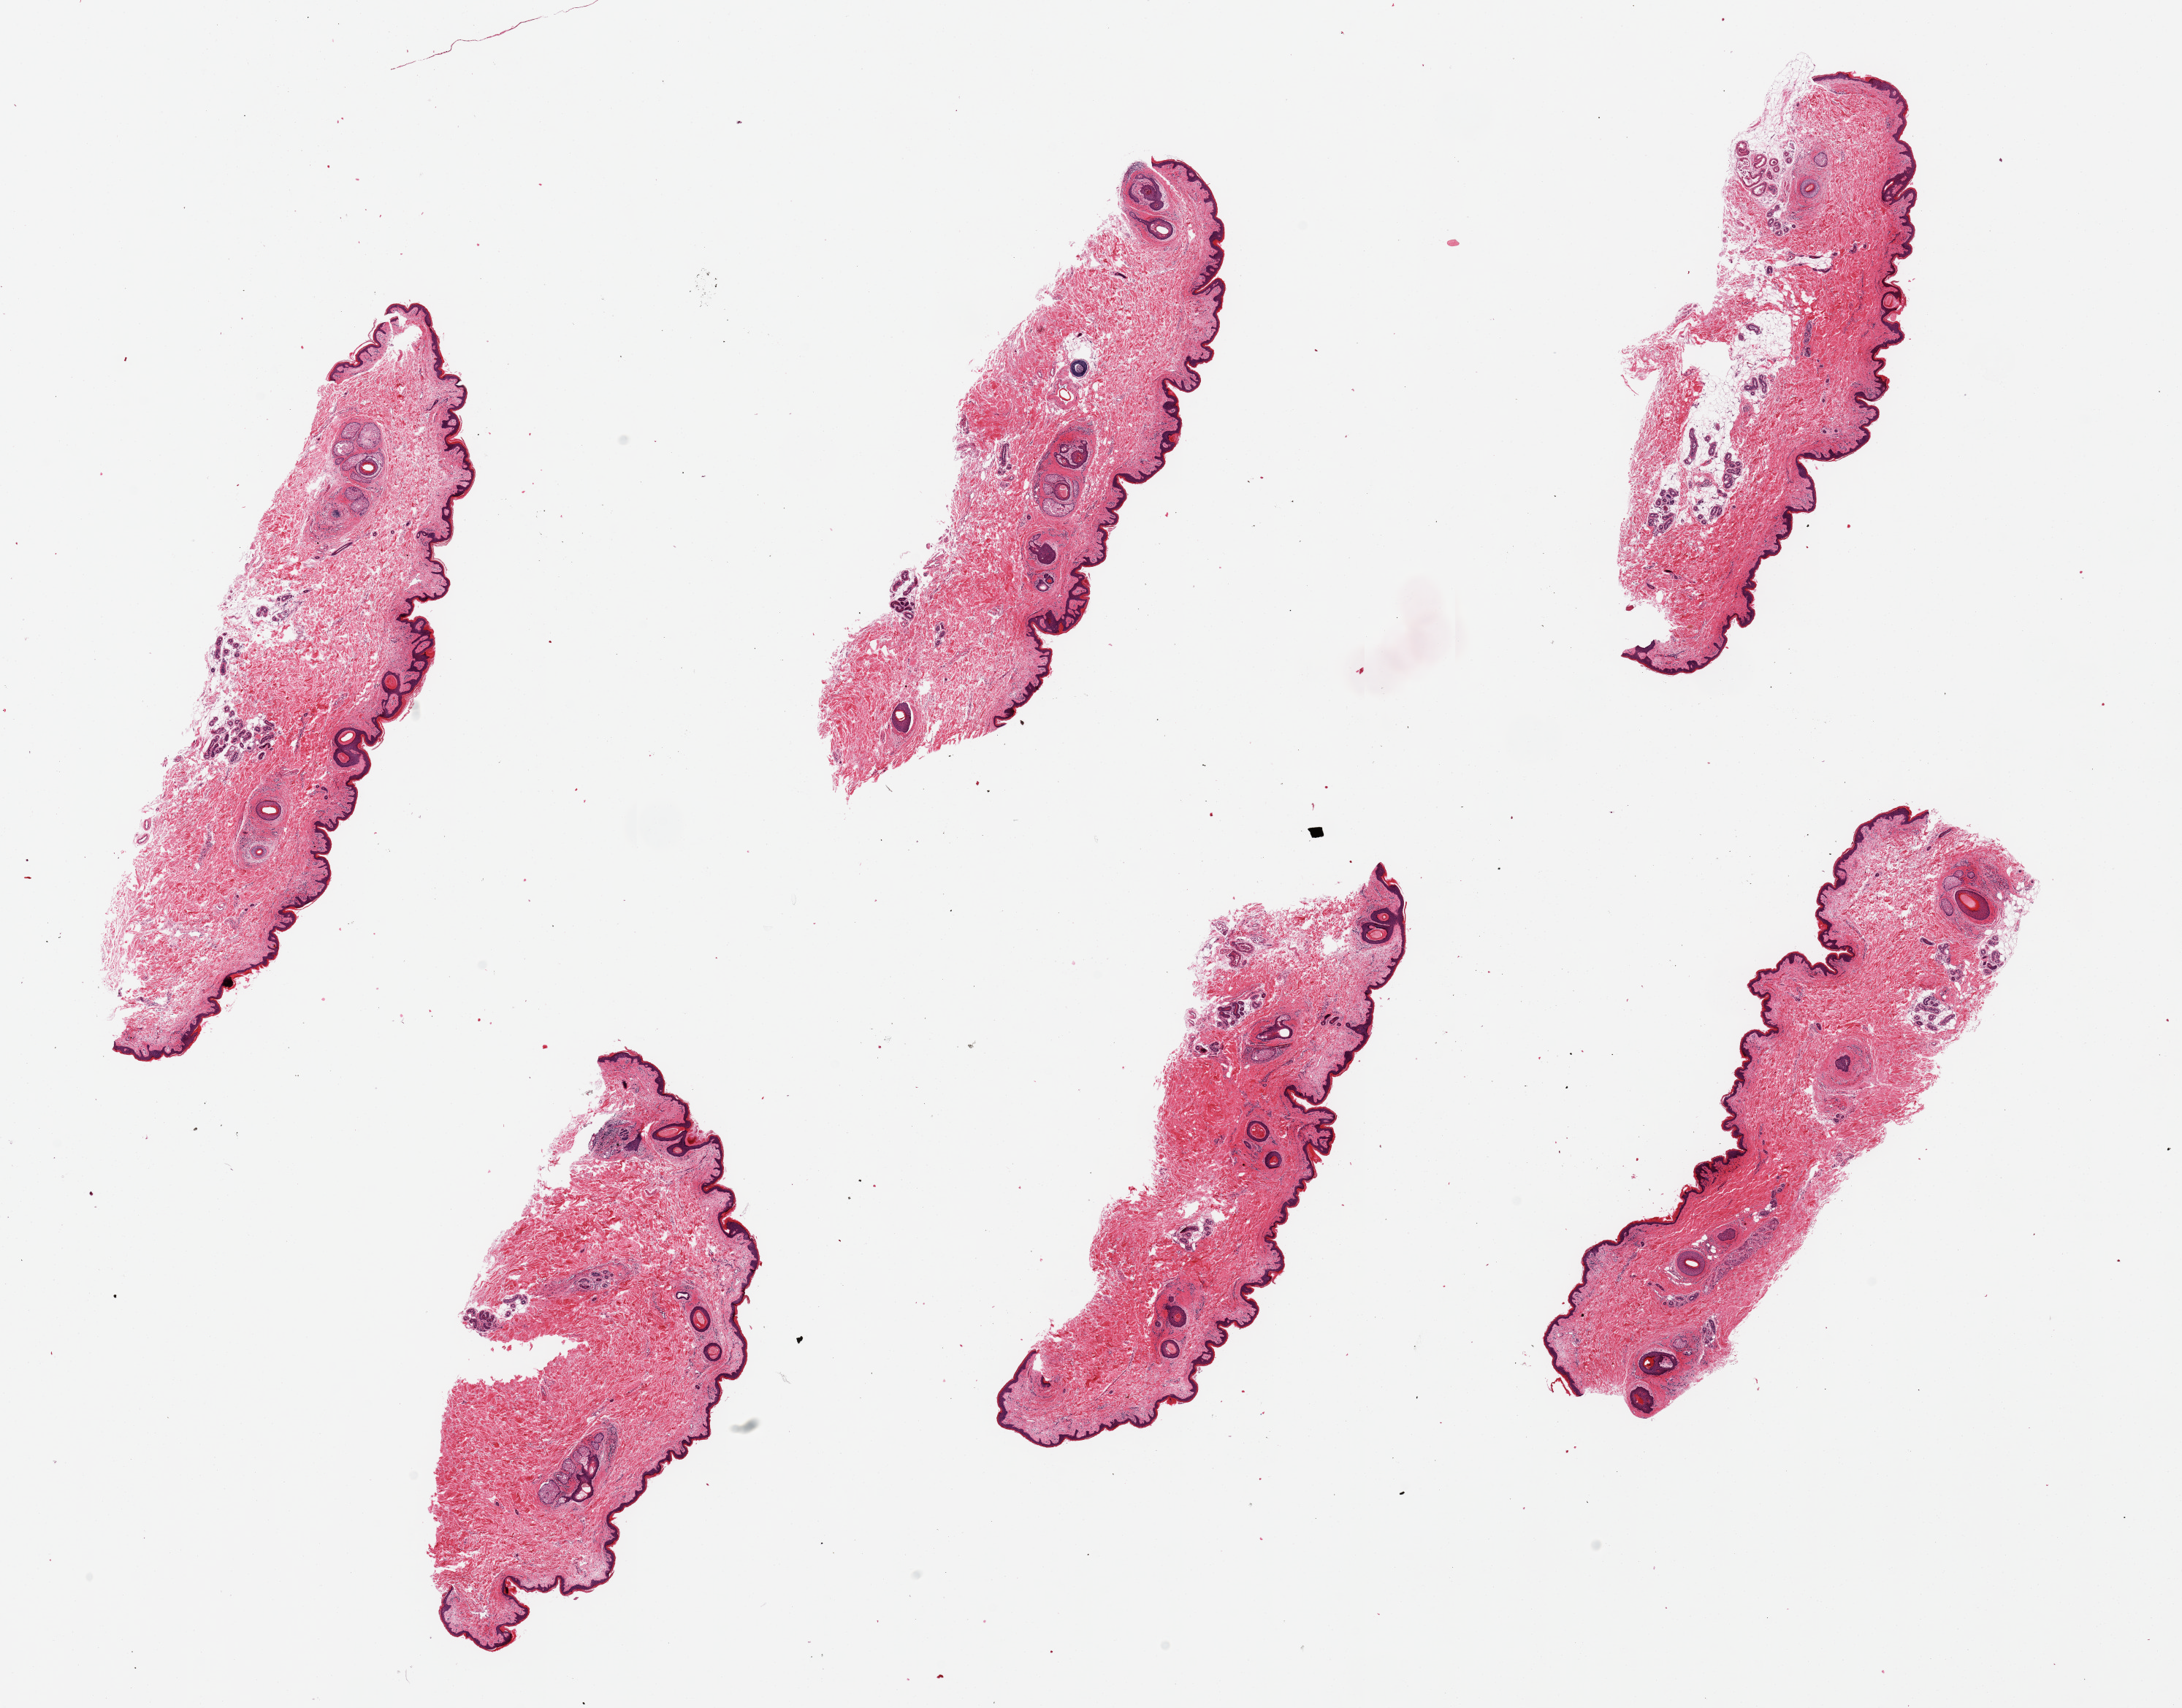
H&E whole-slide image — shown as a low-resolution overview of the whole scanned area (about 23.6 x 18.5 mm); PAXgene-fixed, paraffin-embedded tissue; target tissue: skin of suprapubic region; tissue donor sample. Male donor.
Review note (as recorded): 6 pieces, trace dermal fat; squamous epithelium is ~30-40 microns.